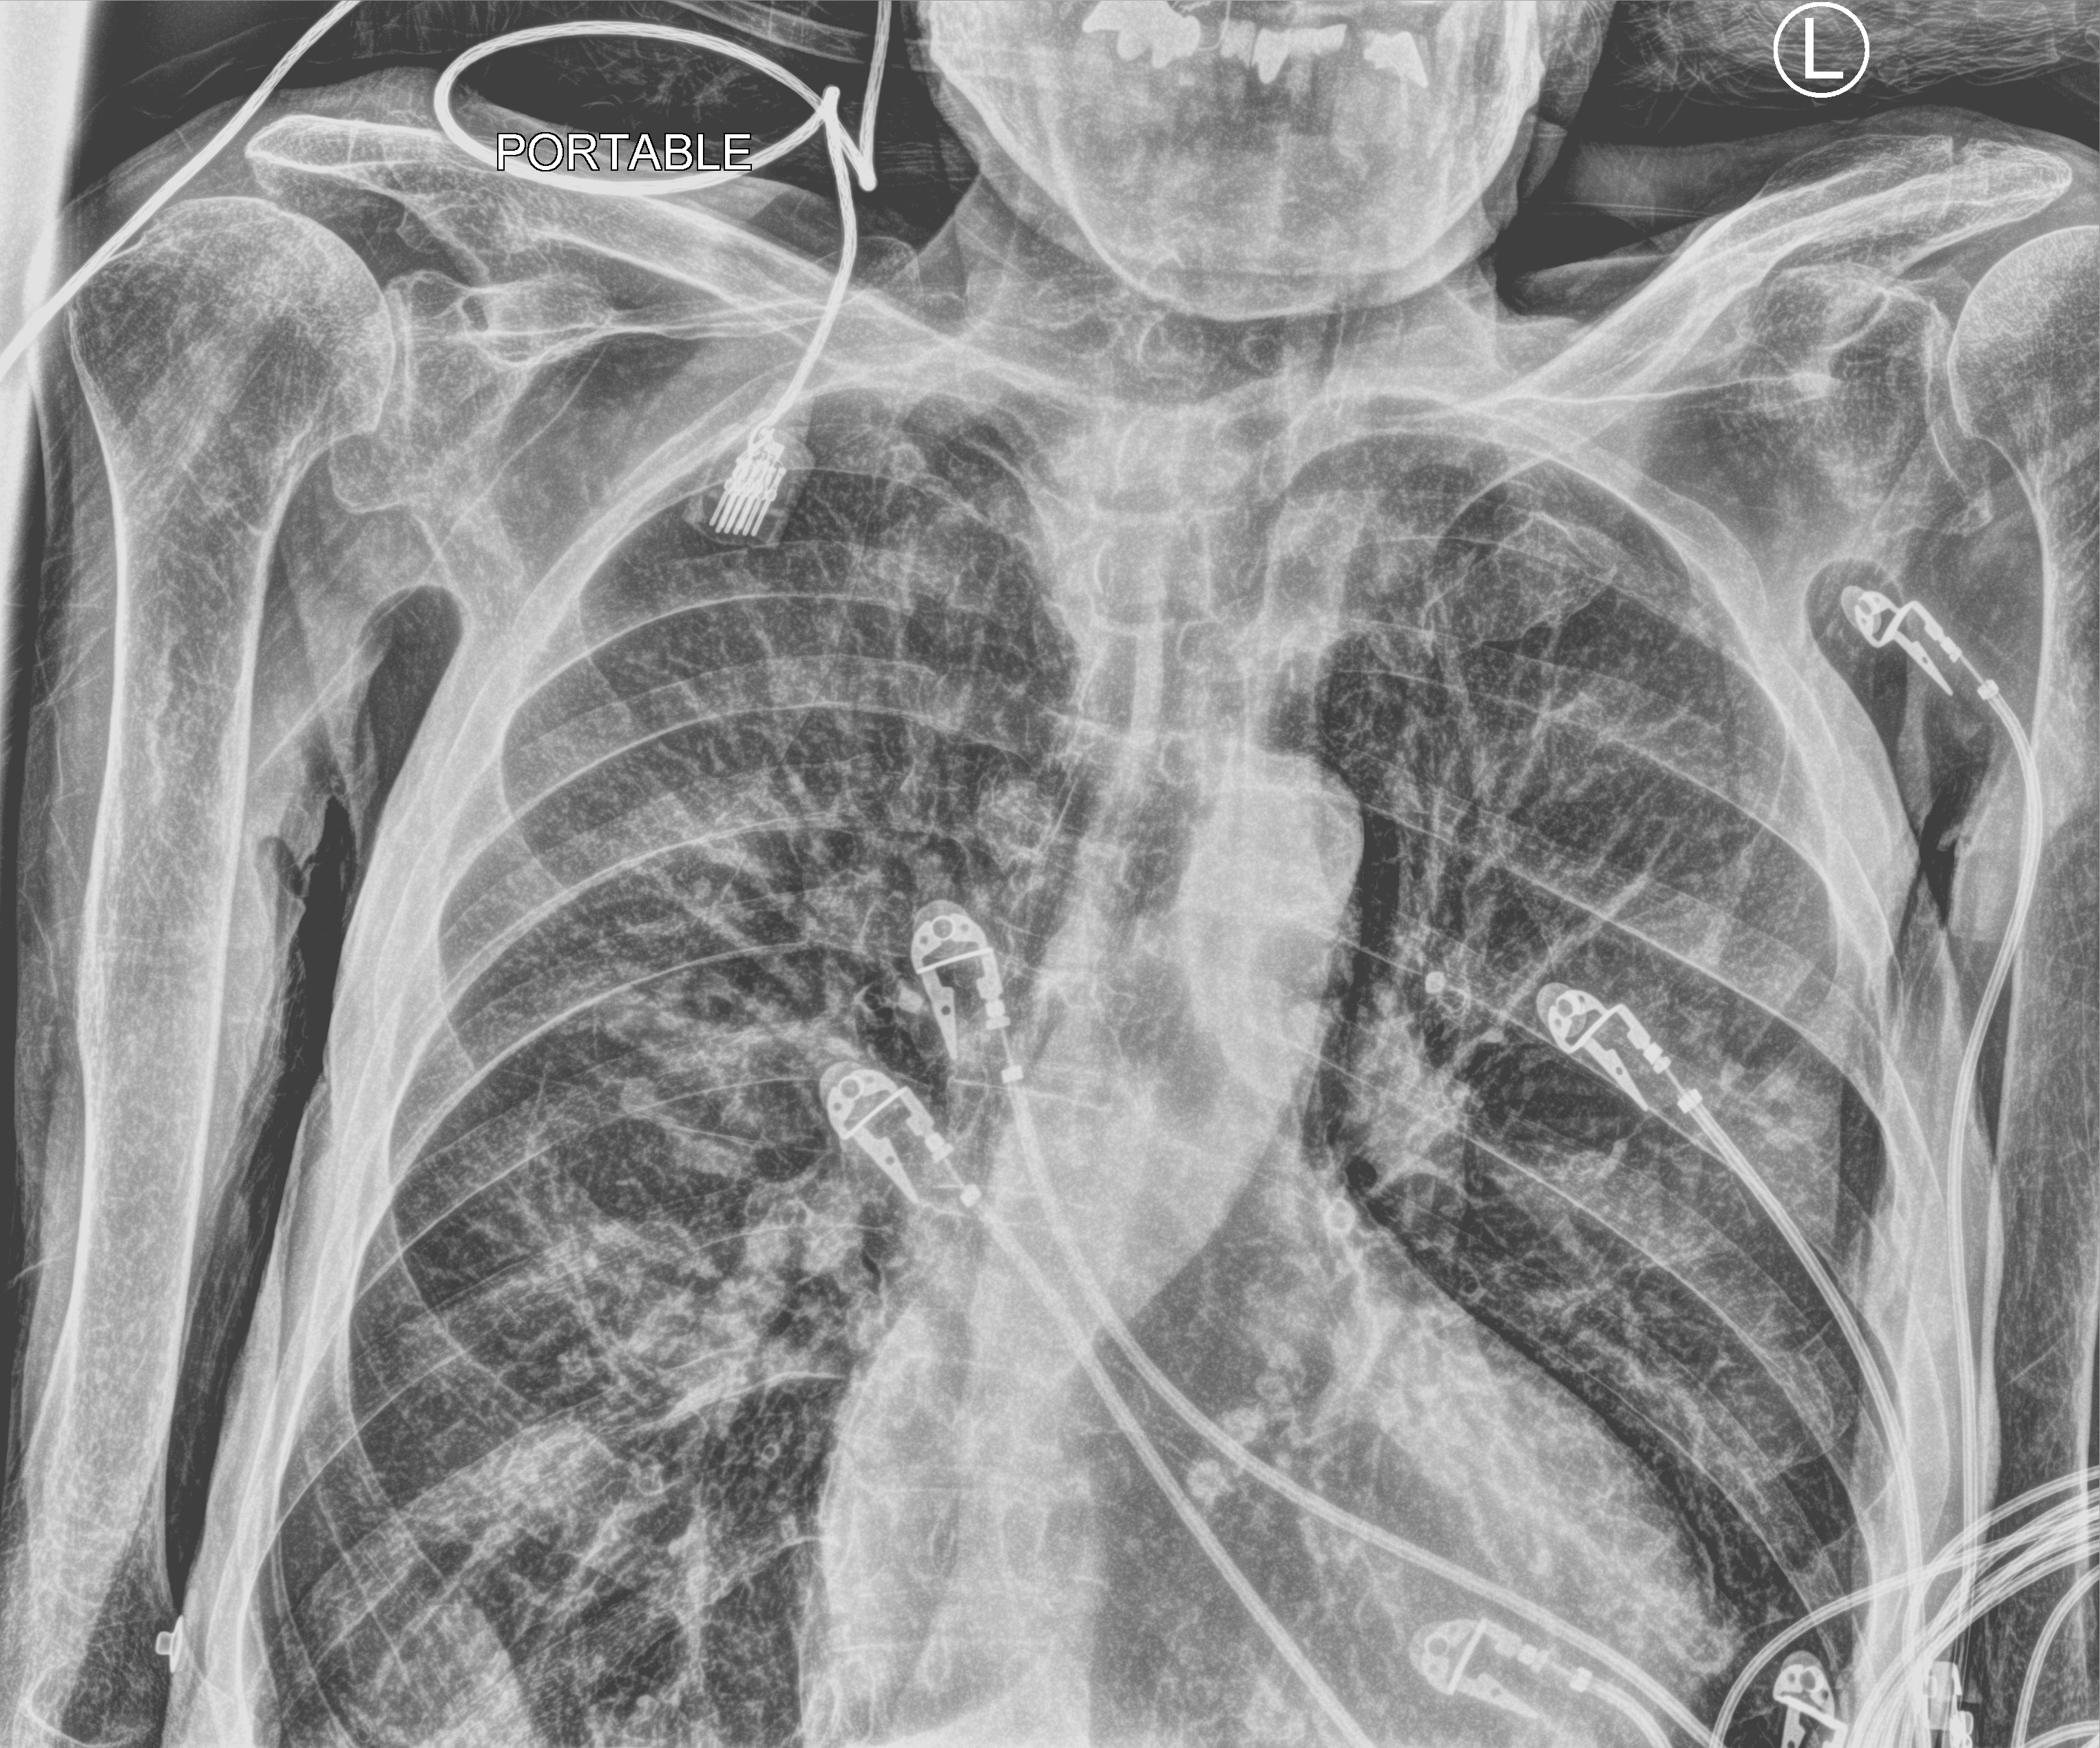
Bedside chest radiograph (computed radiography), anteroposterior (AP) projection. Patient hospitalised with COVID-19; male, aged 75–90 years.
Admission-level facts for this patient (not findings on this image; timing relative to this image not recorded):
- admitted to intensive care during this hospital stay: no